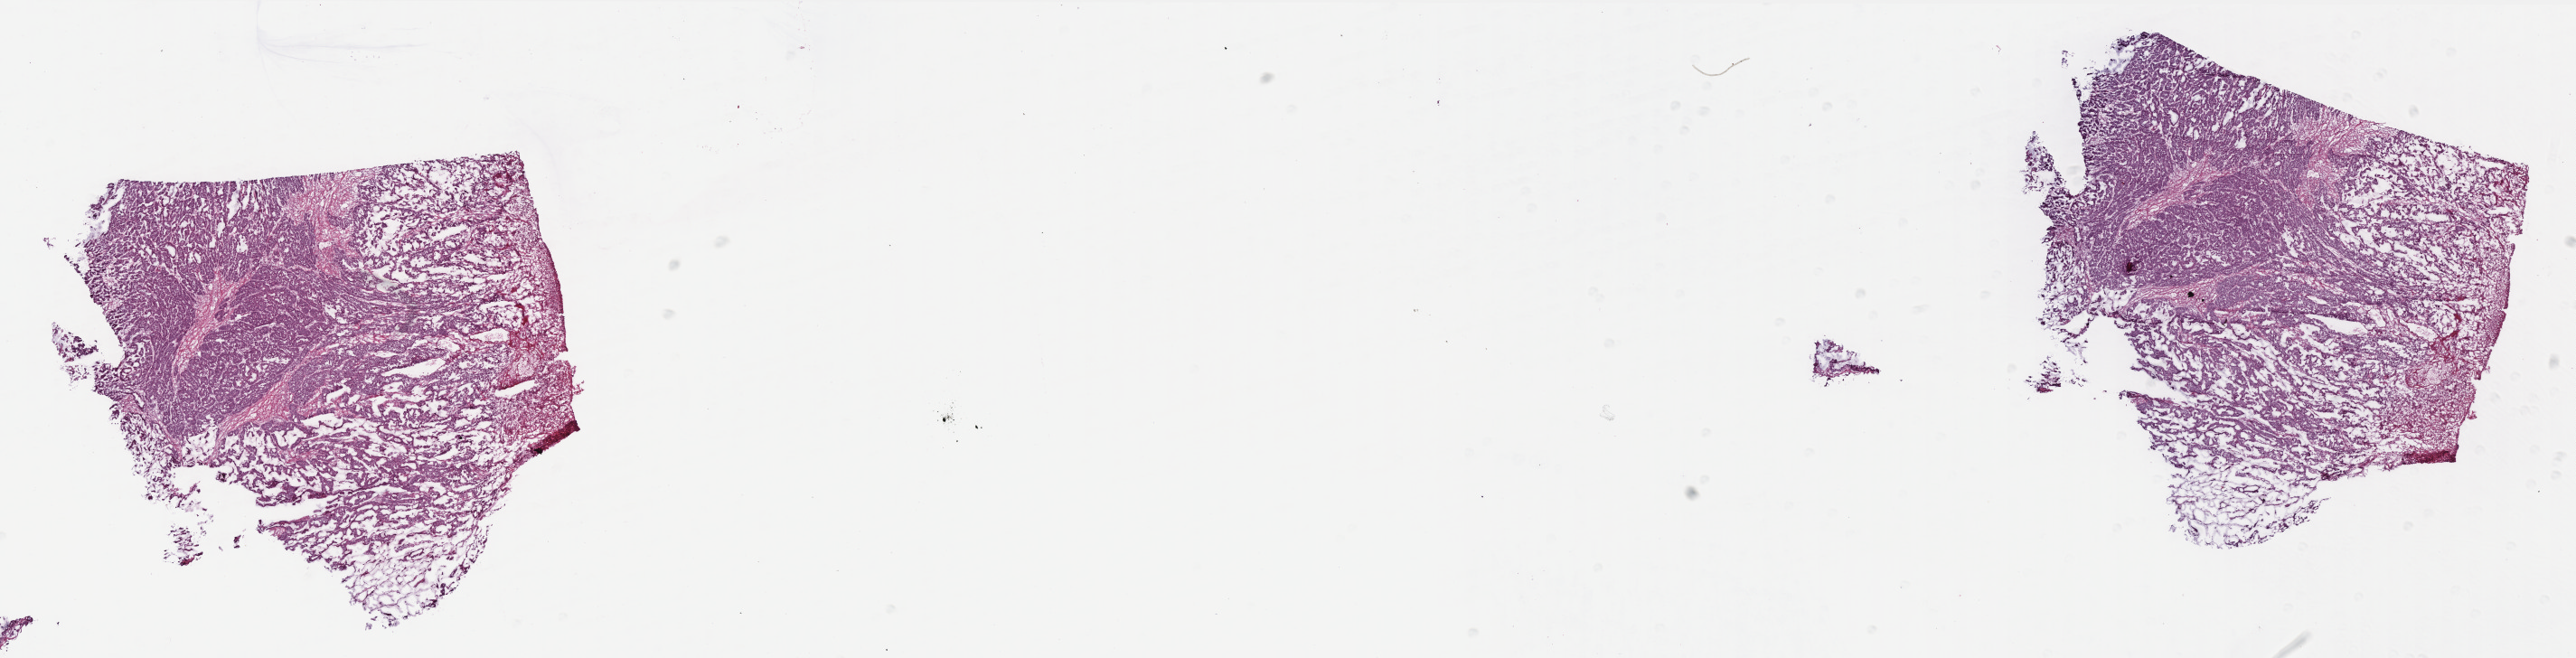
Hematoxylin and eosin (H&E) stained whole-slide image — shown as a low-resolution overview of the whole scanned area (about 22.8 x 5.8 mm, acquisition: 40x scan), frozen section, colon, primary tumour sample. Male patient; age at initial diagnosis 80 years. Composition of this section per pathologist review: tumour cells 87%, tumour nuclei 75%, normal cells 0%, stromal cells 5%, necrosis 8%. Inflammatory infiltration, as recorded: lymphocyte infiltration 1%, monocyte infiltration 1%, neutrophil infiltration 20%.
Lymph nodes positive (case pathology): 2 of 24 examined. AJCC pathologic stage: IIIB (6th edition). TNM: T4 N1 M0. Histologic diagnosis: Mucinous adenocarcinoma (ascending colon).